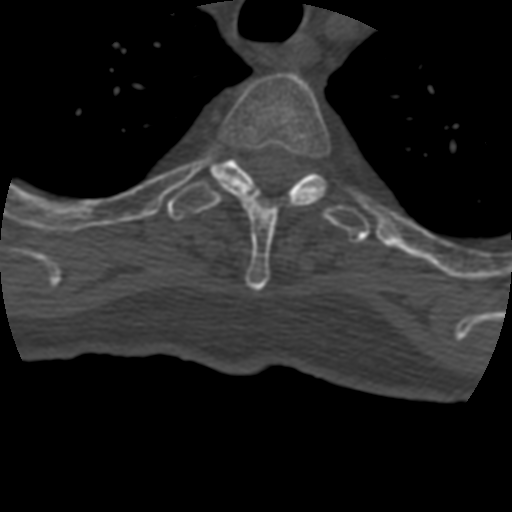
CT including the spine, one axial slice. Position 346 of 399 along the scan axis. Reconstruction kernel STANDARD. 120 kVp. Bone window (W 1800 / L 400 HU). 512 × 512 image matrix. Patient age 69 years. From the clinical record (not read from this slice): primary cancer: prostate.
Outlined on this slice (semi-automatically segmented with operator editing):
- T3 vertebra: bounding box (x1, y1, x2, y2) in pixels: (212, 73, 331, 291)
- T4 vertebra: (167, 158, 372, 243)